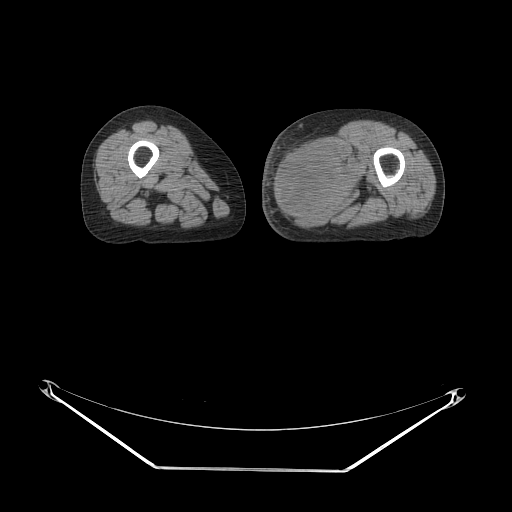
CT of an extremity soft-tissue mass (from a PET/CT study), one axial slice. Slice 24 of 91 in the series (ordered by position). Reconstruction kernel STANDARD. 140 kVp. Soft-tissue window (W 400 / L 40 HU). 3.75 mm slice thickness. 512 × 512 image matrix, field of view 500 × 500 mm. Female patient. From the clinical record (not read from this slice): histological type: pleomorphic leiomyosarcoma; grade: high; site of the primary tumour: left thigh.
Outlined on this slice (expert contour drawn on MRI and transferred to this co-registered scan by the dataset authors):
- gross tumour volume including surrounding oedema: box from (x=272, y=135) to (x=359, y=216) px
- gross tumour volume (mass): (x=272, y=144)–(x=353, y=216)